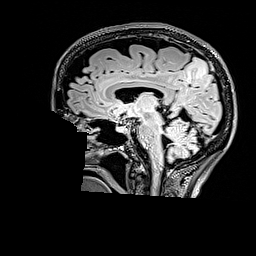
Brain MRI from a brain-tumour surgery series, one sagittal slice. Position 95 of 176 along the scan axis. T2 FLAIR. 1 mm slice thickness. 256 × 256 image matrix, field of view 256 × 256 mm. Case-level facts recorded for this patient, not image findings: histopathology: Astrocytoma; WHO grade: 3; IDH mutation: yes; tumour location: Right Parietal.
Annotated regions visible in this slice (outlined manually by an expert reader):
- tumour: bounding box [x1, y1, x2, y2] px = [184, 56, 208, 82]
- tumour: [184, 57, 207, 81]